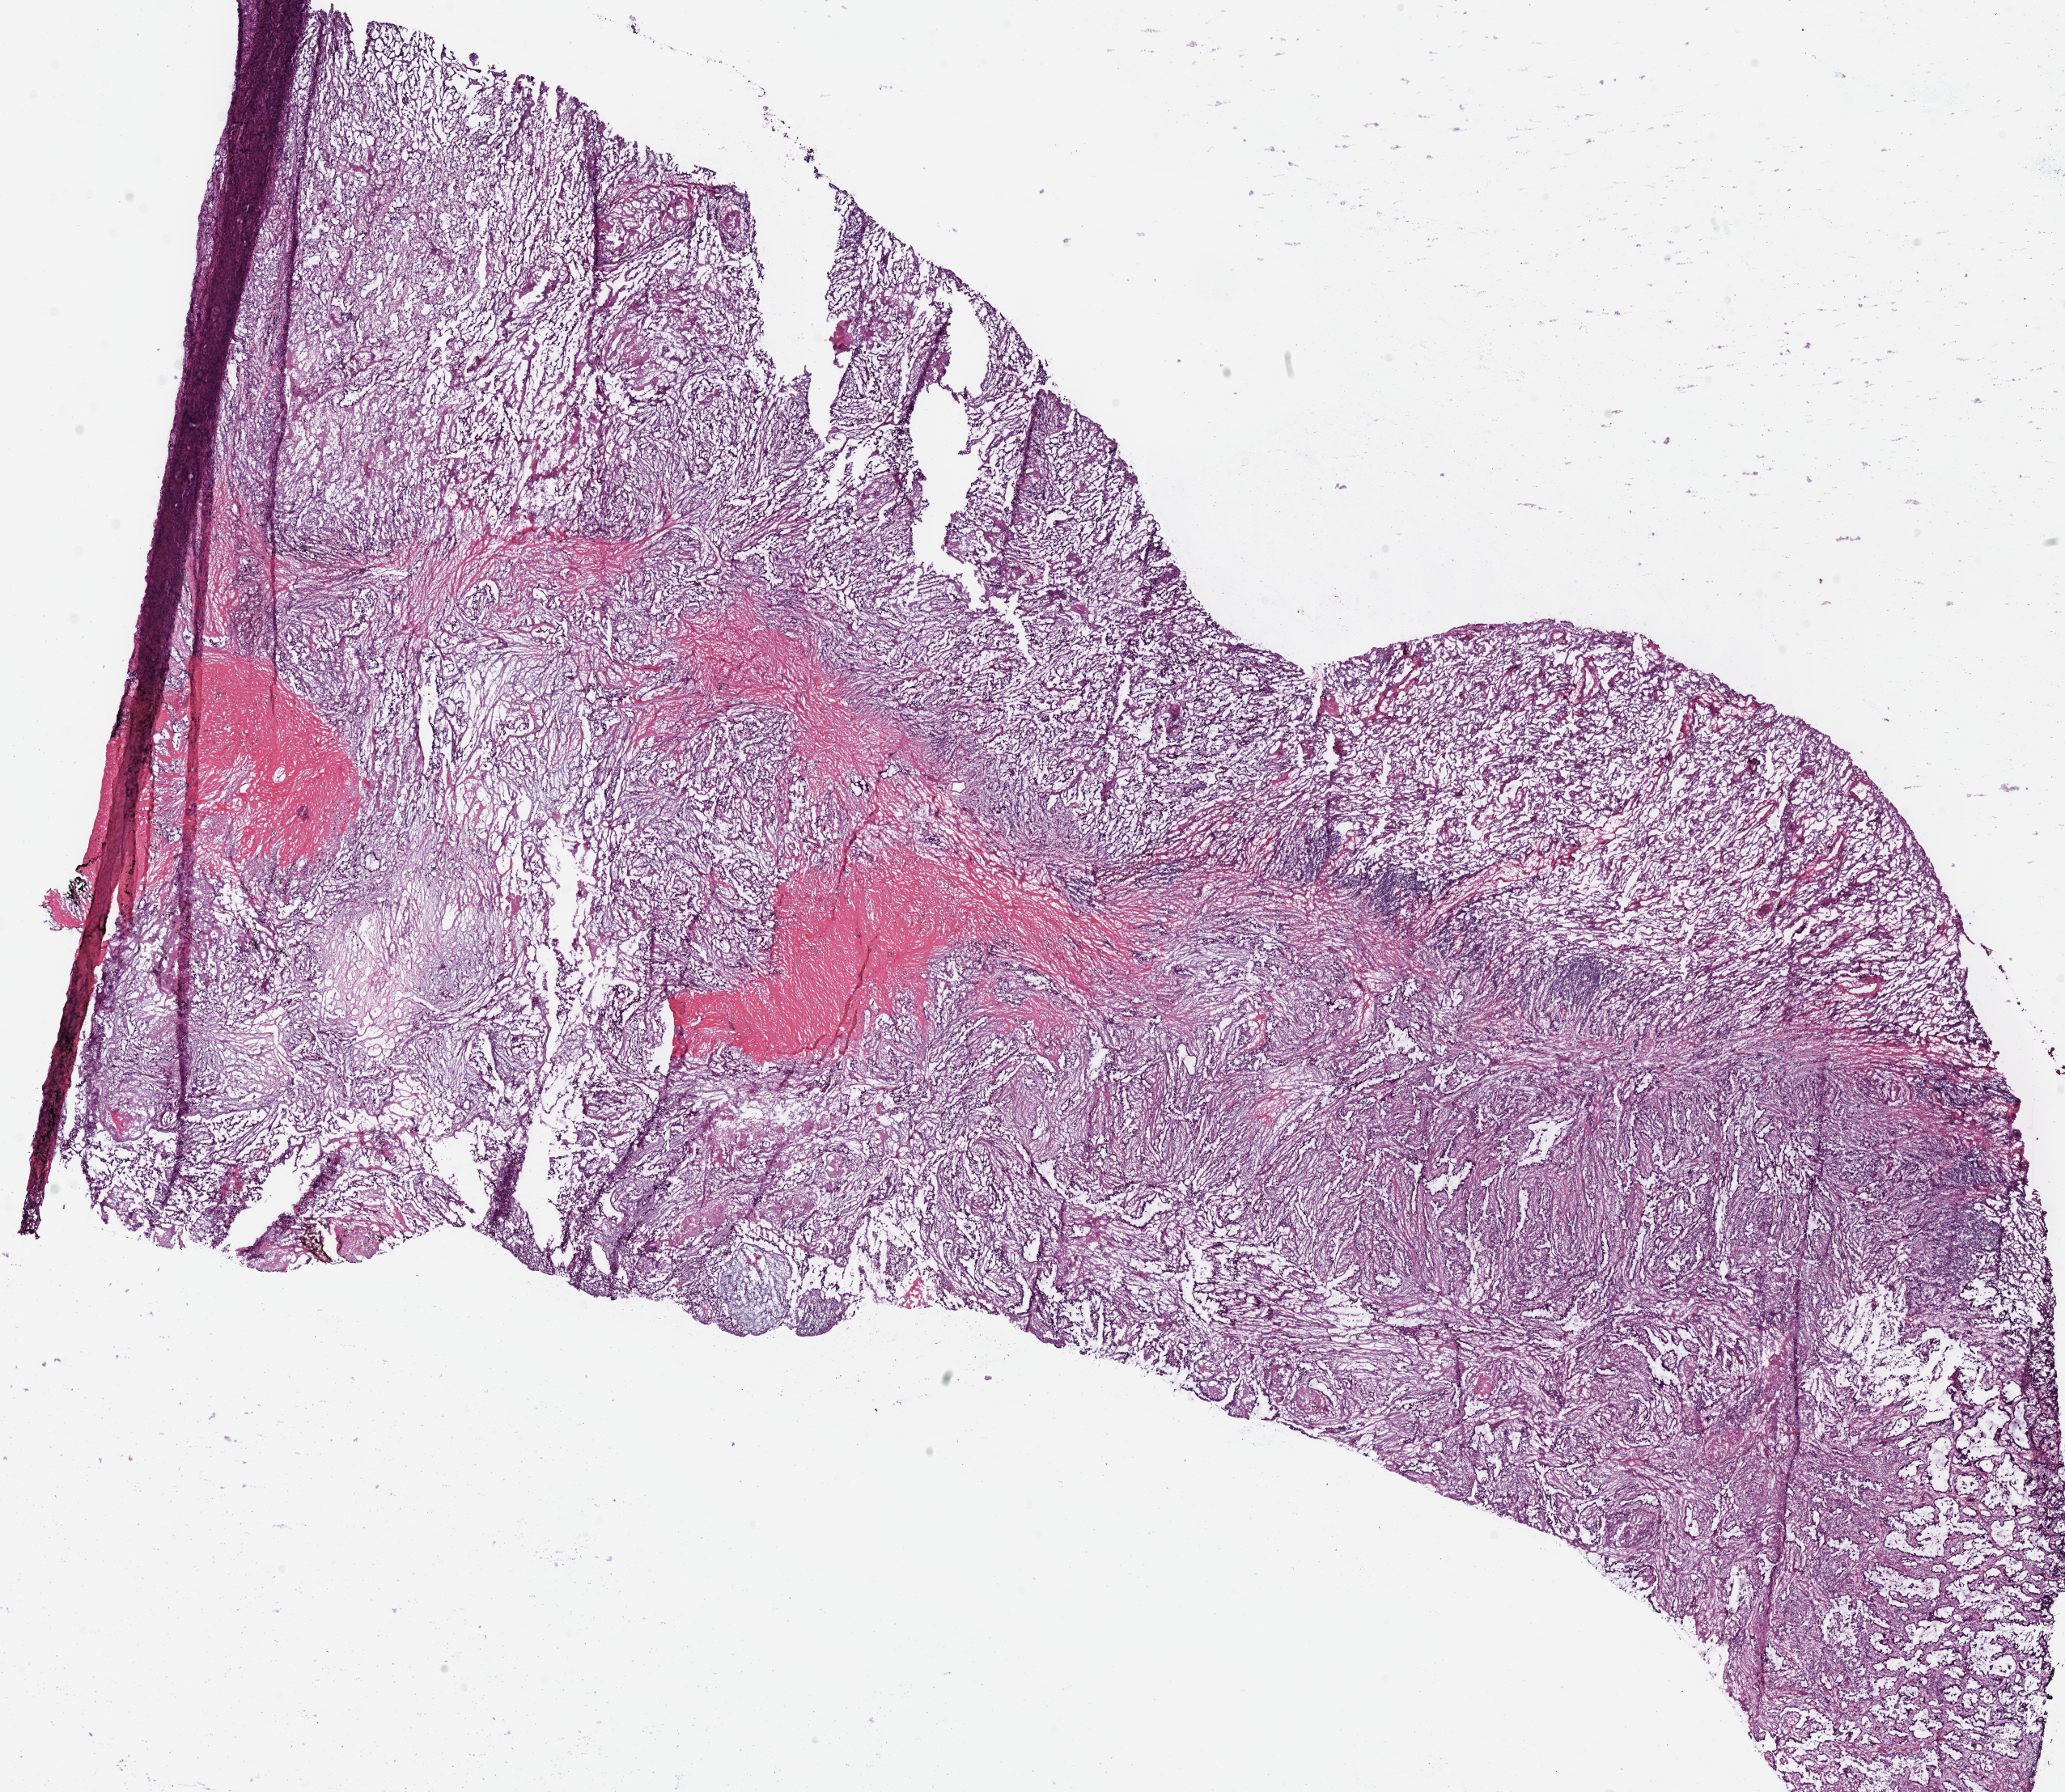
Whole-slide histology image, H&E — low-resolution overview of the scanned area, about 20.1 x 17.4 mm (acquisition: 40x scan). Frozen section from the top of the tissue portion. Sample: primary tumour, lung. Male patient; age at initial diagnosis 79 years. Composition of this section per pathologist review: tumour cells 40%, tumour nuclei 60%.
Pathologic diagnosis: Adenocarcinoma, NOS.